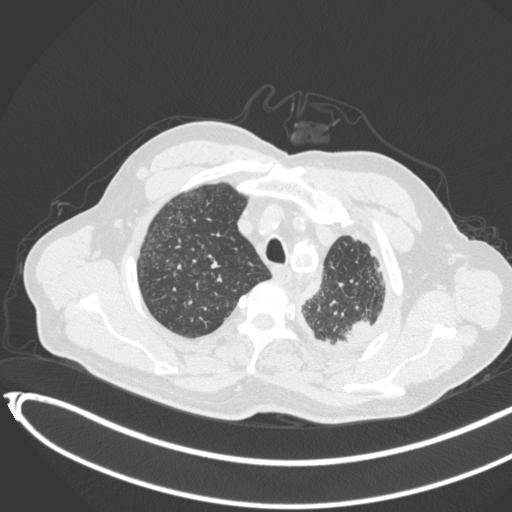
Chest CT, one axial slice; position 360 of 451 along the scan axis; lung window (W 1500 / L -600 HU); 1 mm slice thickness; 512 × 512 image matrix. Male patient, age 78 years. From the clinical record (not read from this slice): clinical TNM (as recorded): T1c N0 M1.
Structures marked on this image (rectangle marked by the reading radiologist):
- lung tumour (recorded histology: adenocarcinoma): bounding box (x1, y1, x2, y2) in pixels: (345, 315, 374, 344)